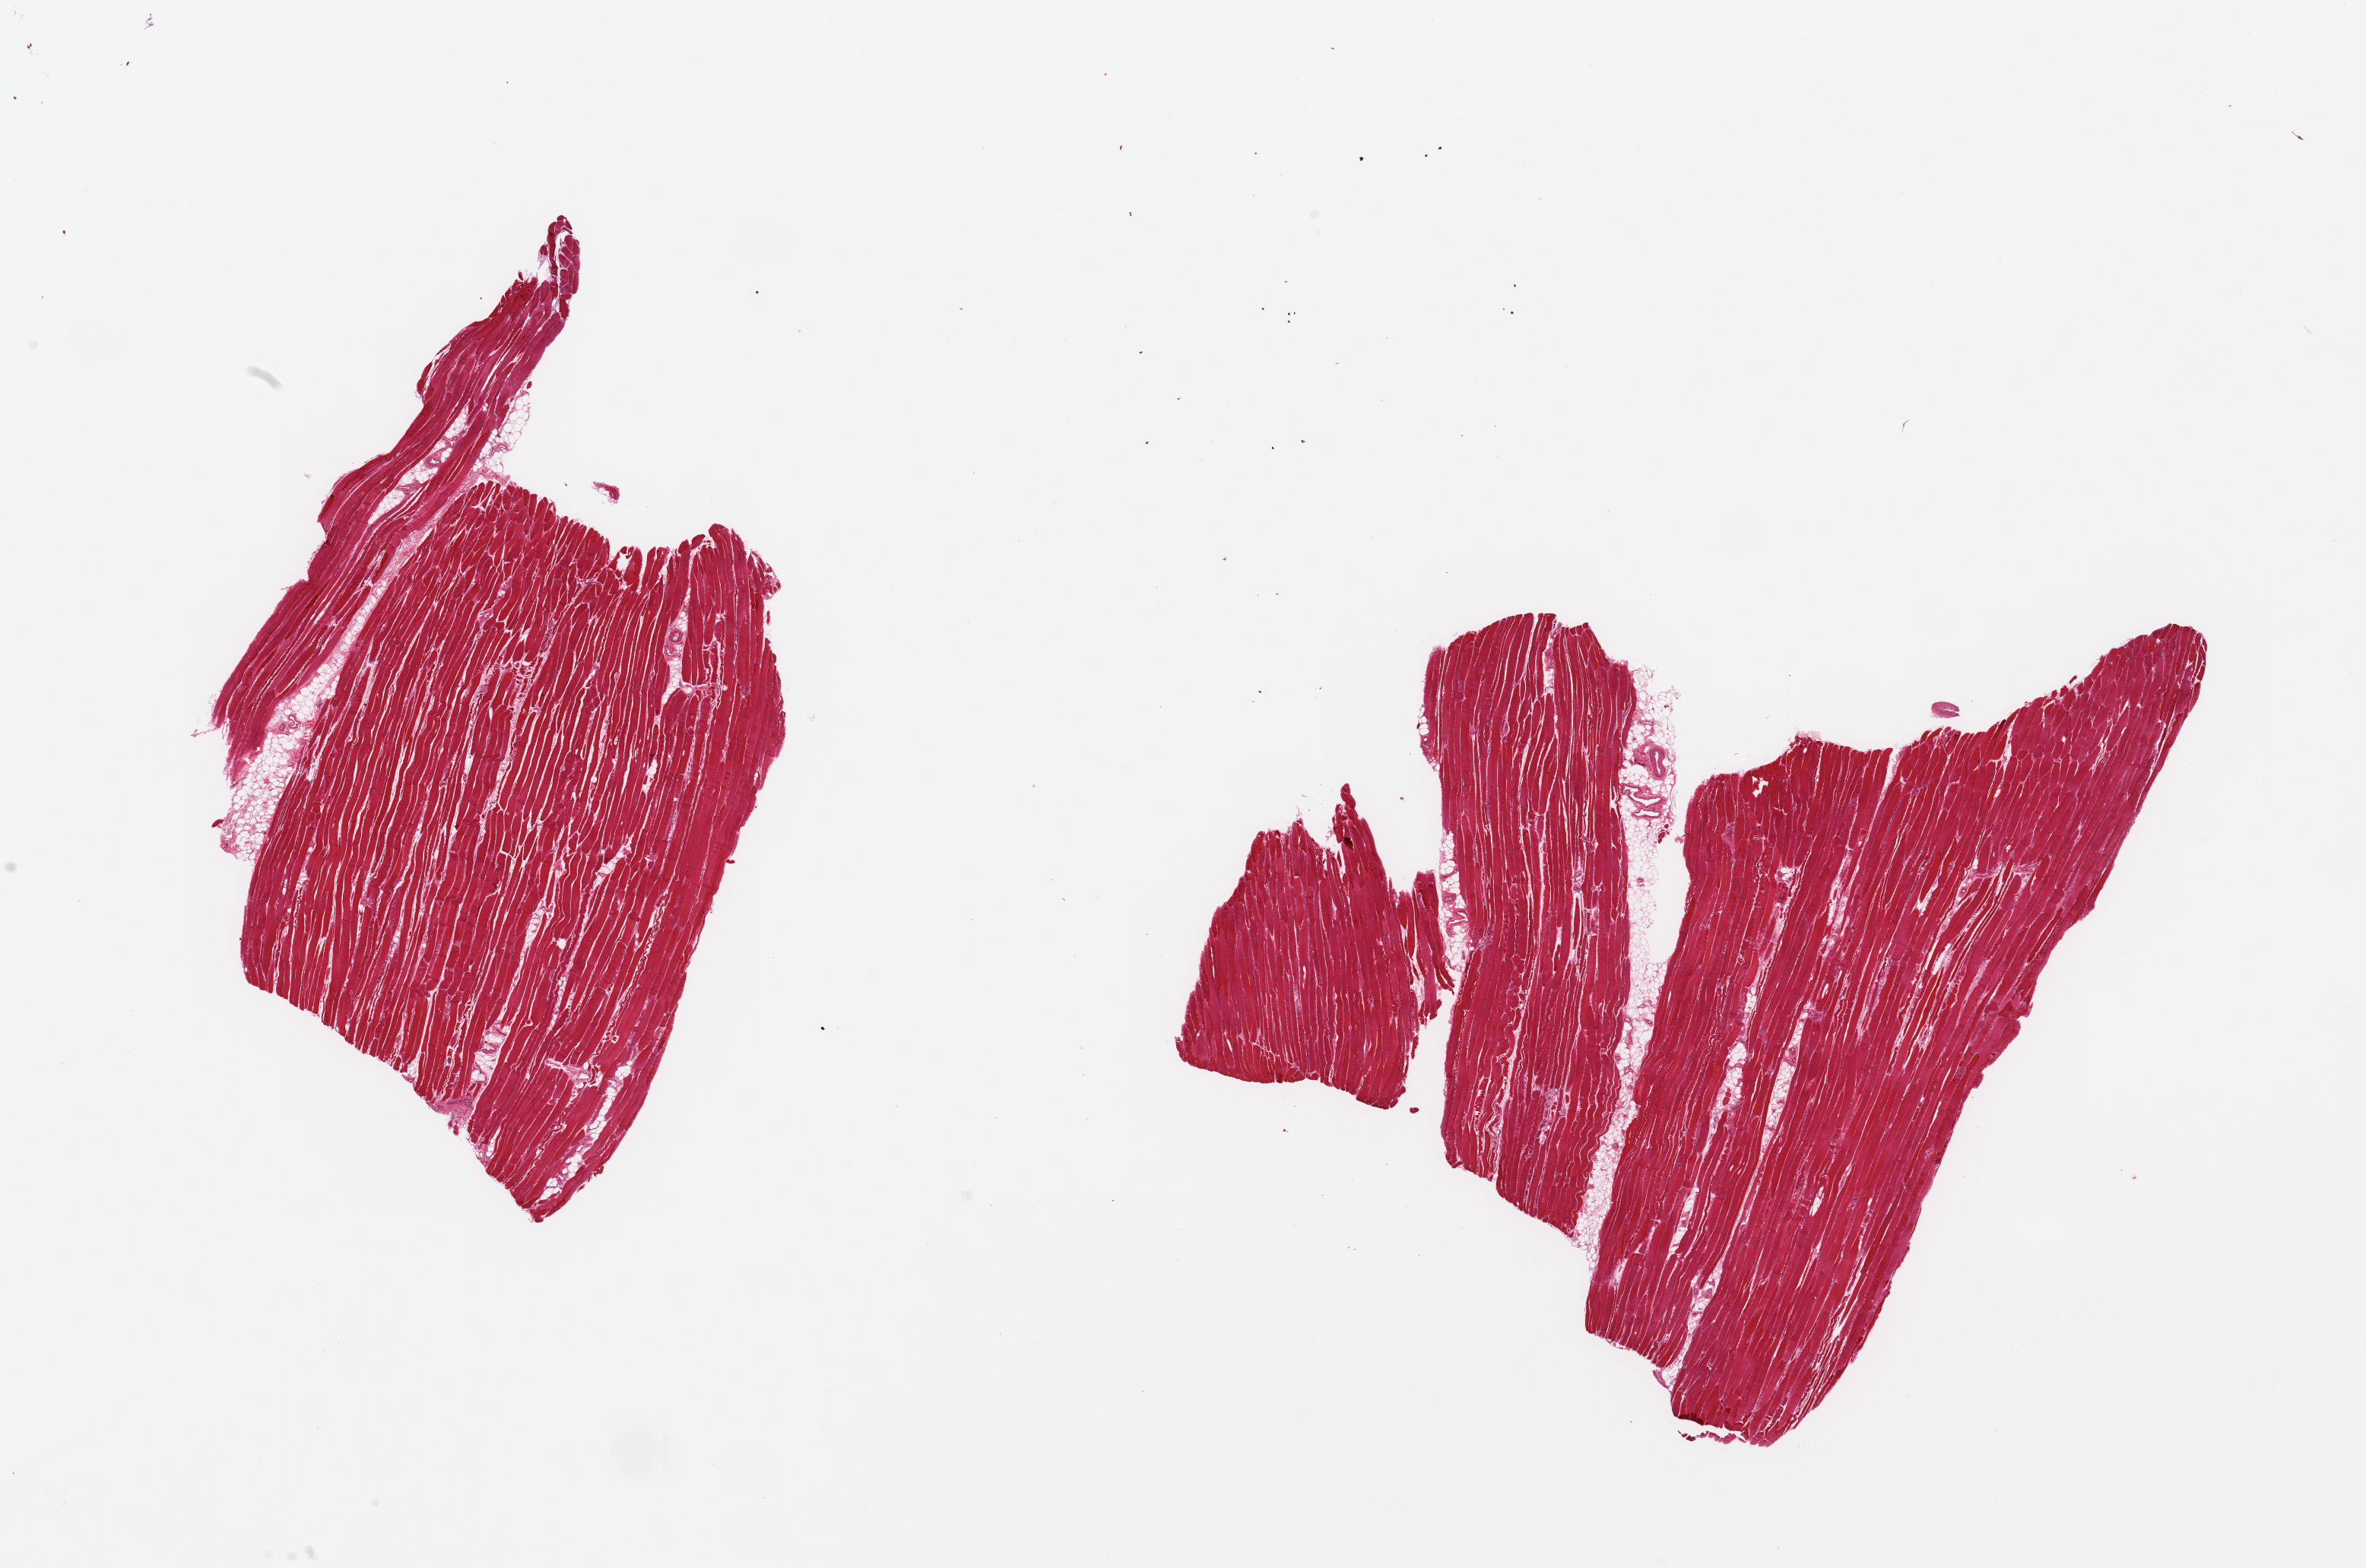
Haematoxylin and eosin whole-slide image, shown as a low-resolution overview of the whole scanned area (about 24.6 x 16.3 mm, acquisition: 20x scan); PAXgene-fixed paraffin-embedded (PFPE) section; target tissue: skeletal muscle; donor tissue sample. Male donor.
Reviewer comment on this tissue sample: 2 pieces, ~10% interstial fat.